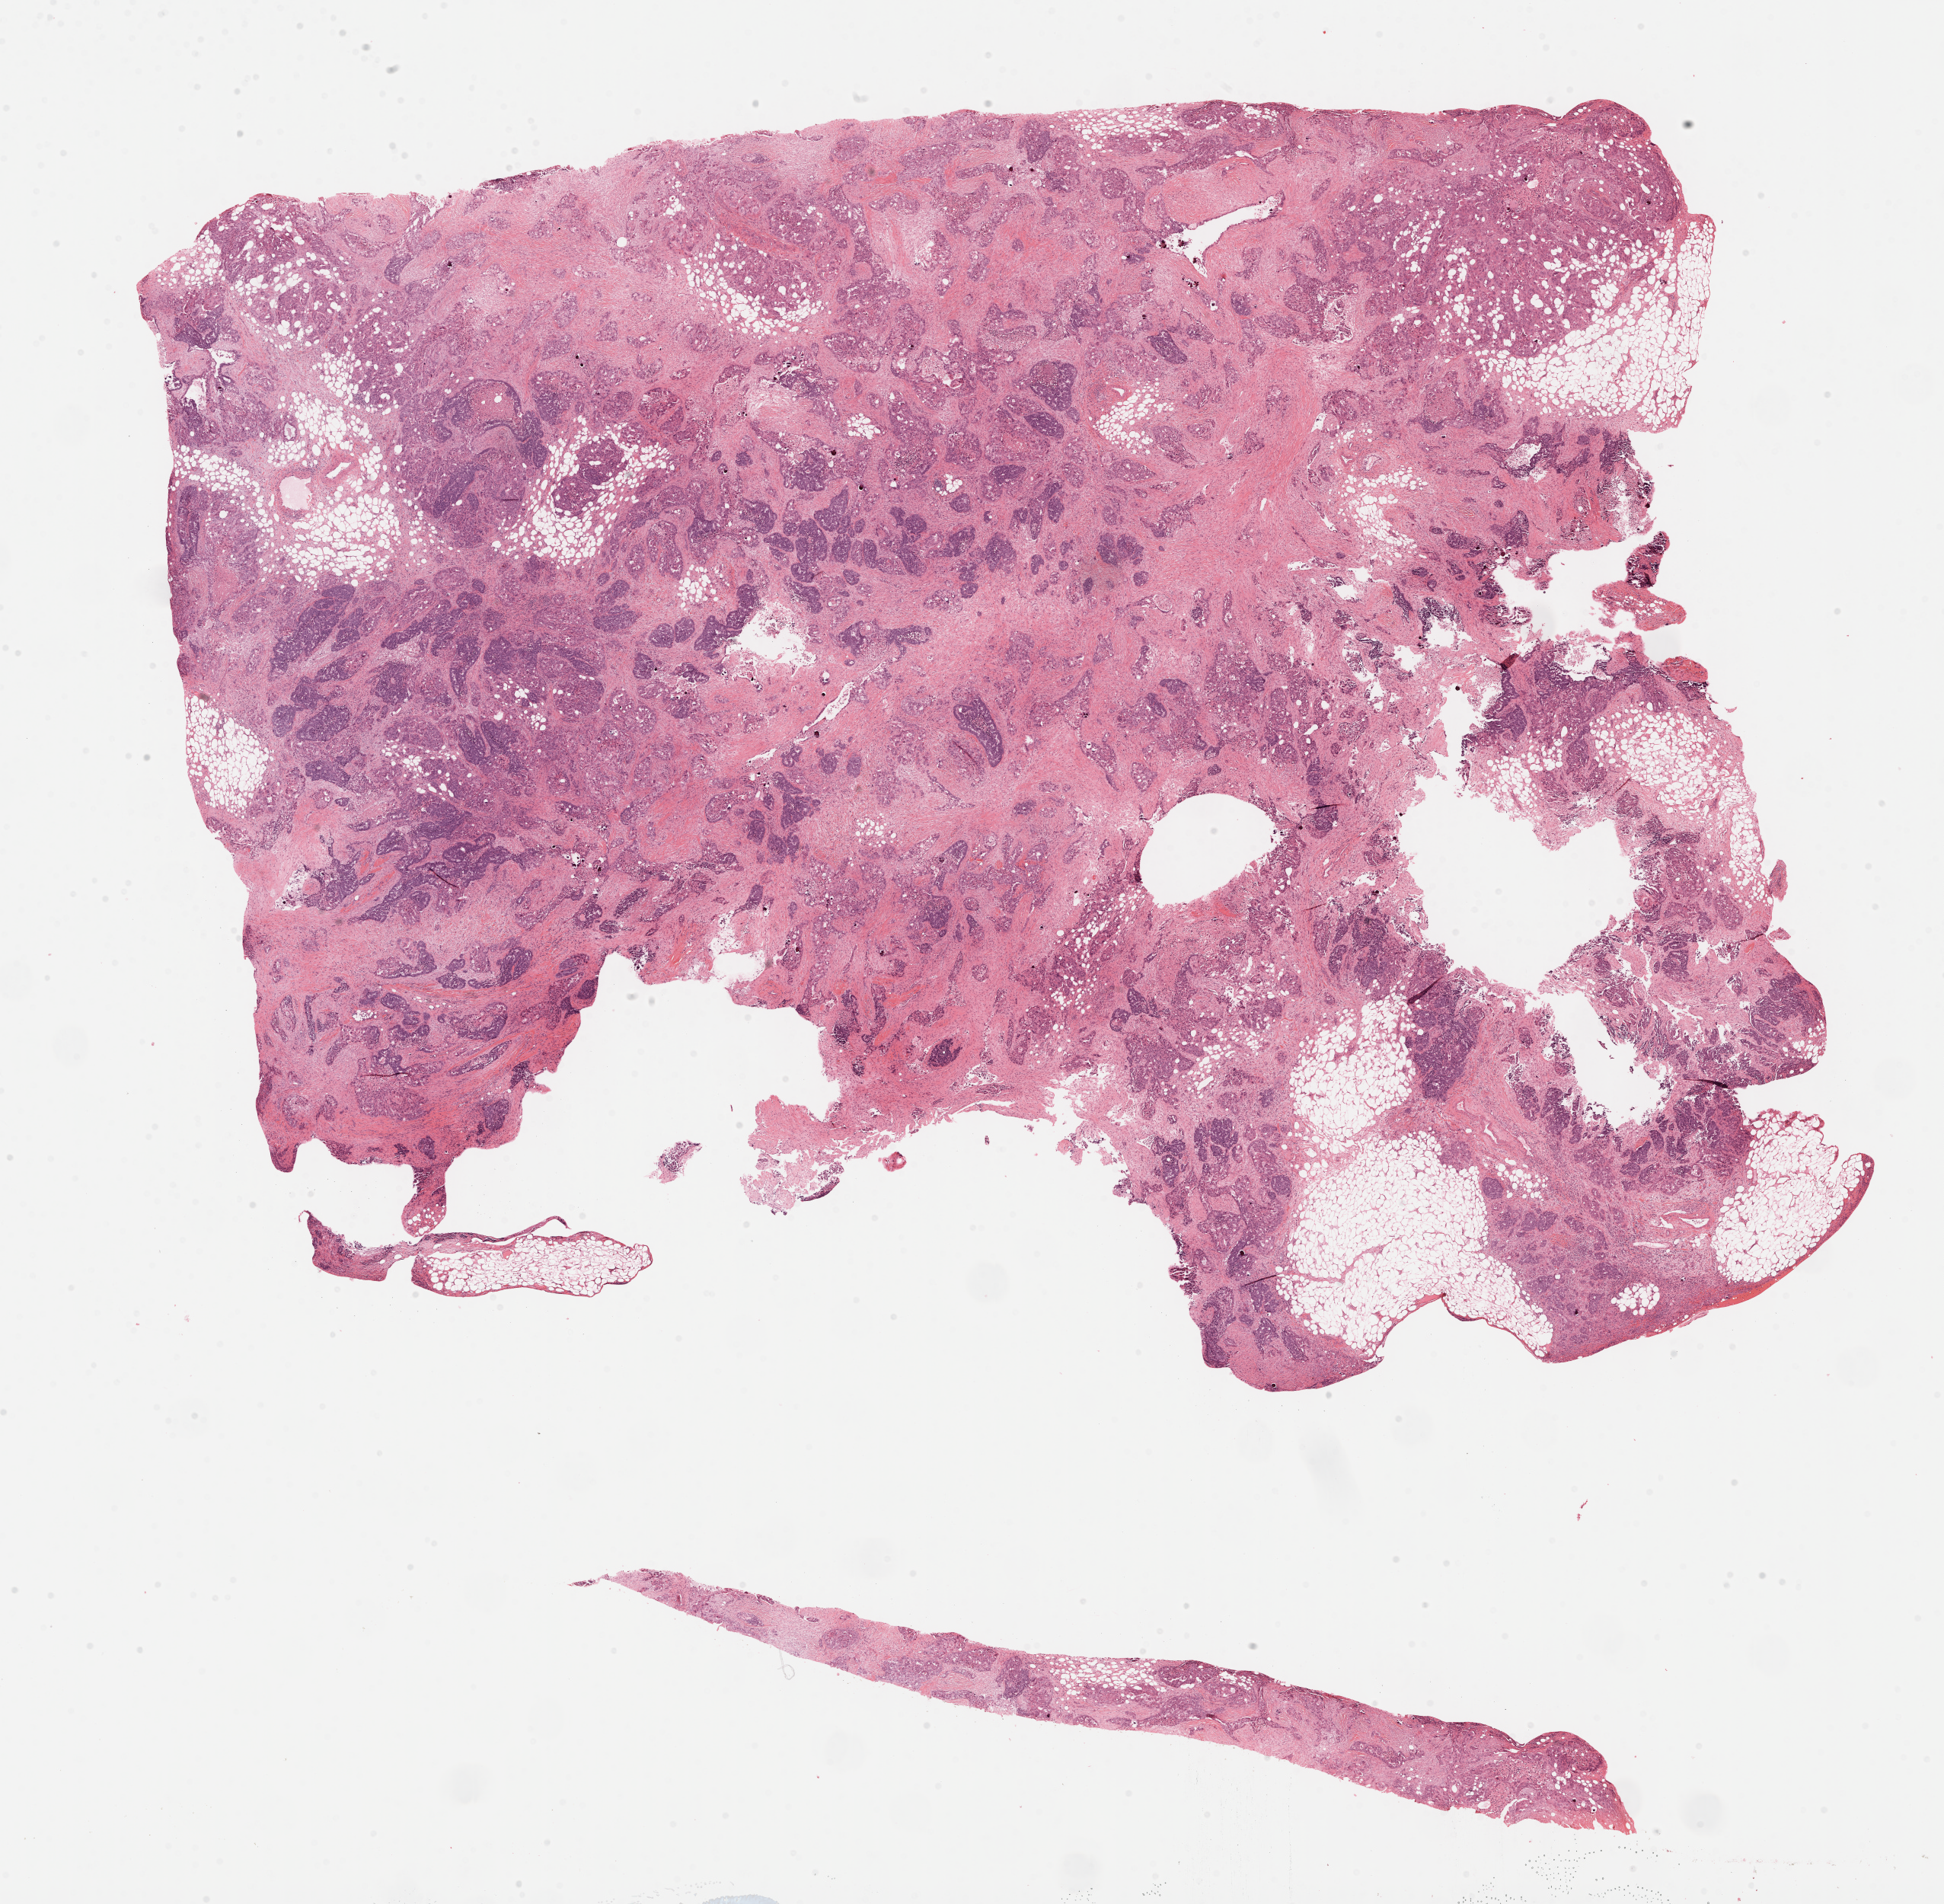
Whole-slide histology image, H&E — low-resolution overview of the scanned area, about 20.6 x 20.2 mm (acquisition: 40x scan); FFPE section; primary tumour sample from the ovary. Patient: female, age at initial diagnosis 73 years. Histologic grade: G3 (poorly differentiated).
Pathologic diagnosis: Serous cystadenocarcinoma, NOS. FIGO stage: IIIC.